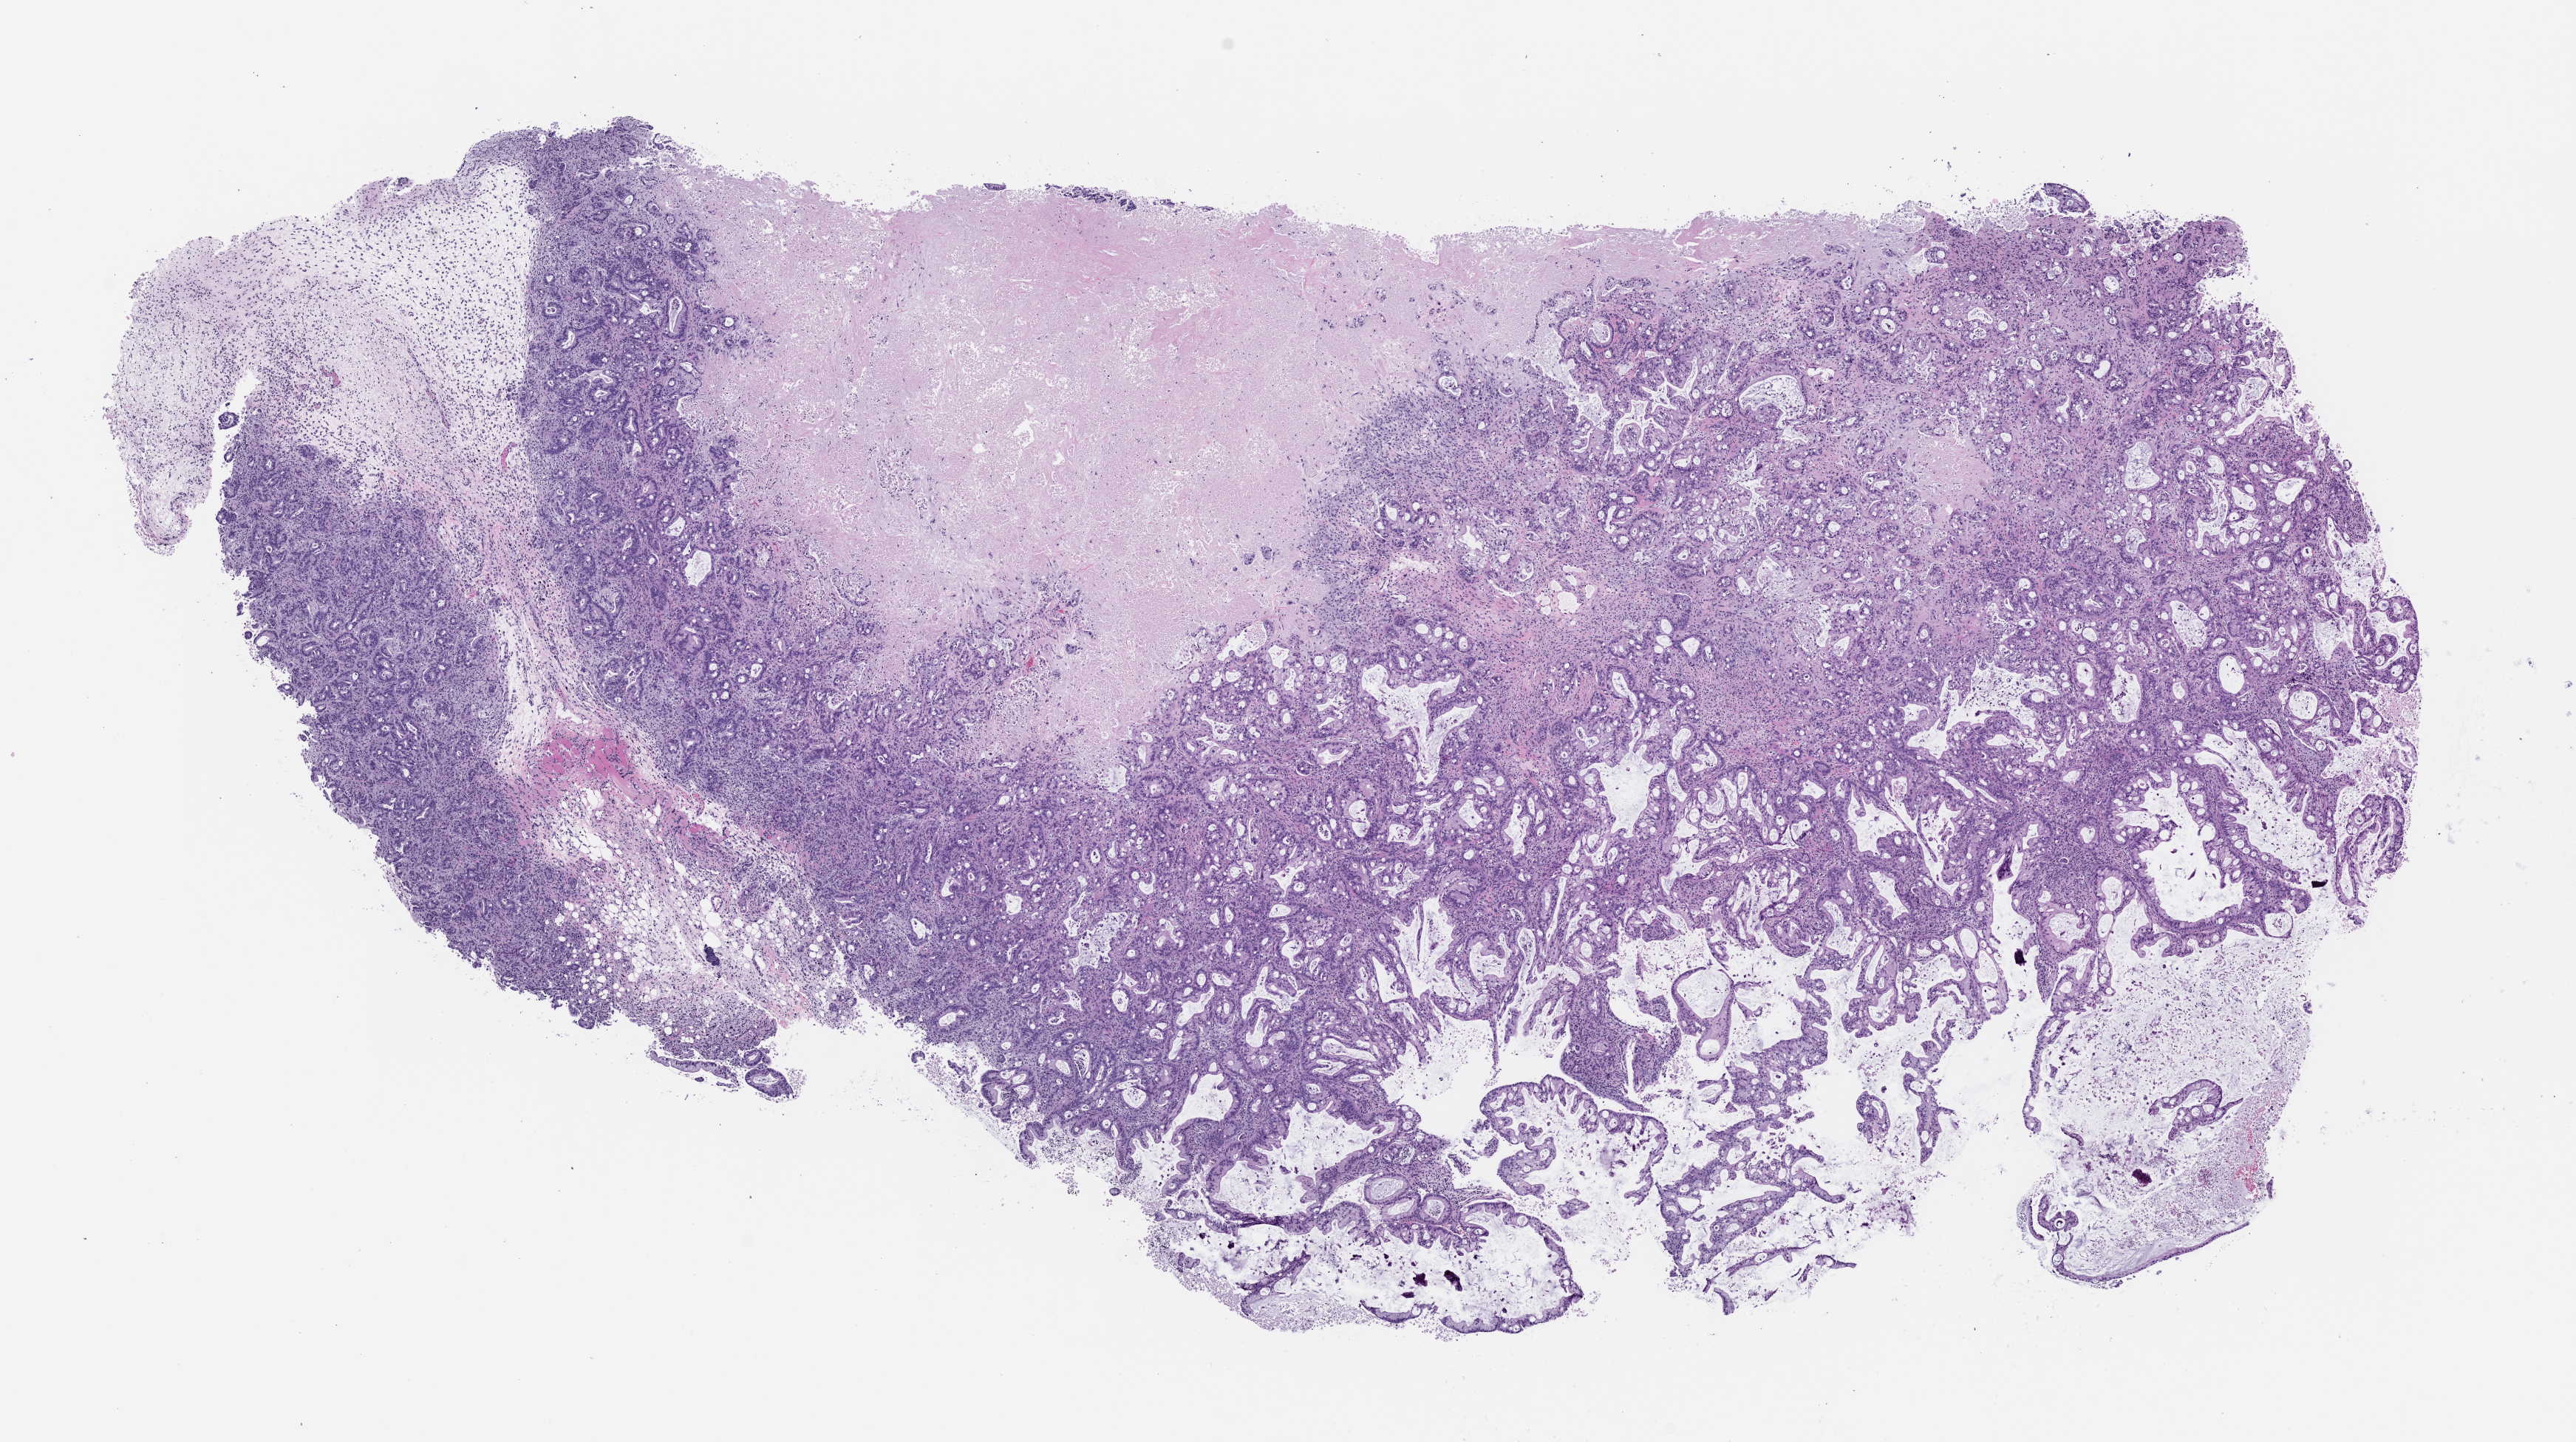
Hematoxylin and eosin (H&E) whole-slide image of a patient-derived xenograft (PDX) tumor grown in a mouse, passage 1, shown as a low-resolution overview of the whole scanned area (about 14.0 x 7.9 mm), formalin-fixed, paraffin-embedded (FFPE) tissue, originating tumor site category: pancreas.
* originating patient diagnosis: Pancreatic Adenocarcinoma